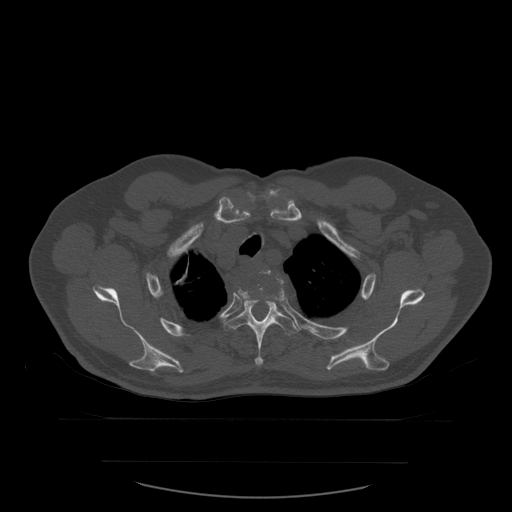
CT including the spine, one axial slice; slice 449 of 590 in the series (ordered by position); bone window (W 1800 / L 400 HU); 1.25 mm slice thickness; 512 × 512 image matrix. Patient age 71 years. From the clinical record (not read from this slice): primary cancer: lung; vertebrae with lytic lesions (as recorded): T1, T2, L5, S1.
Structures marked on this image (semi-automatic segmentation, software-assisted and operator-edited):
- T2 vertebra: bounding box [x1, y1, x2, y2] px = [269, 271, 271, 274]
- T3 vertebra: [238, 271, 285, 299]
- T4 vertebra: [225, 283, 299, 367]